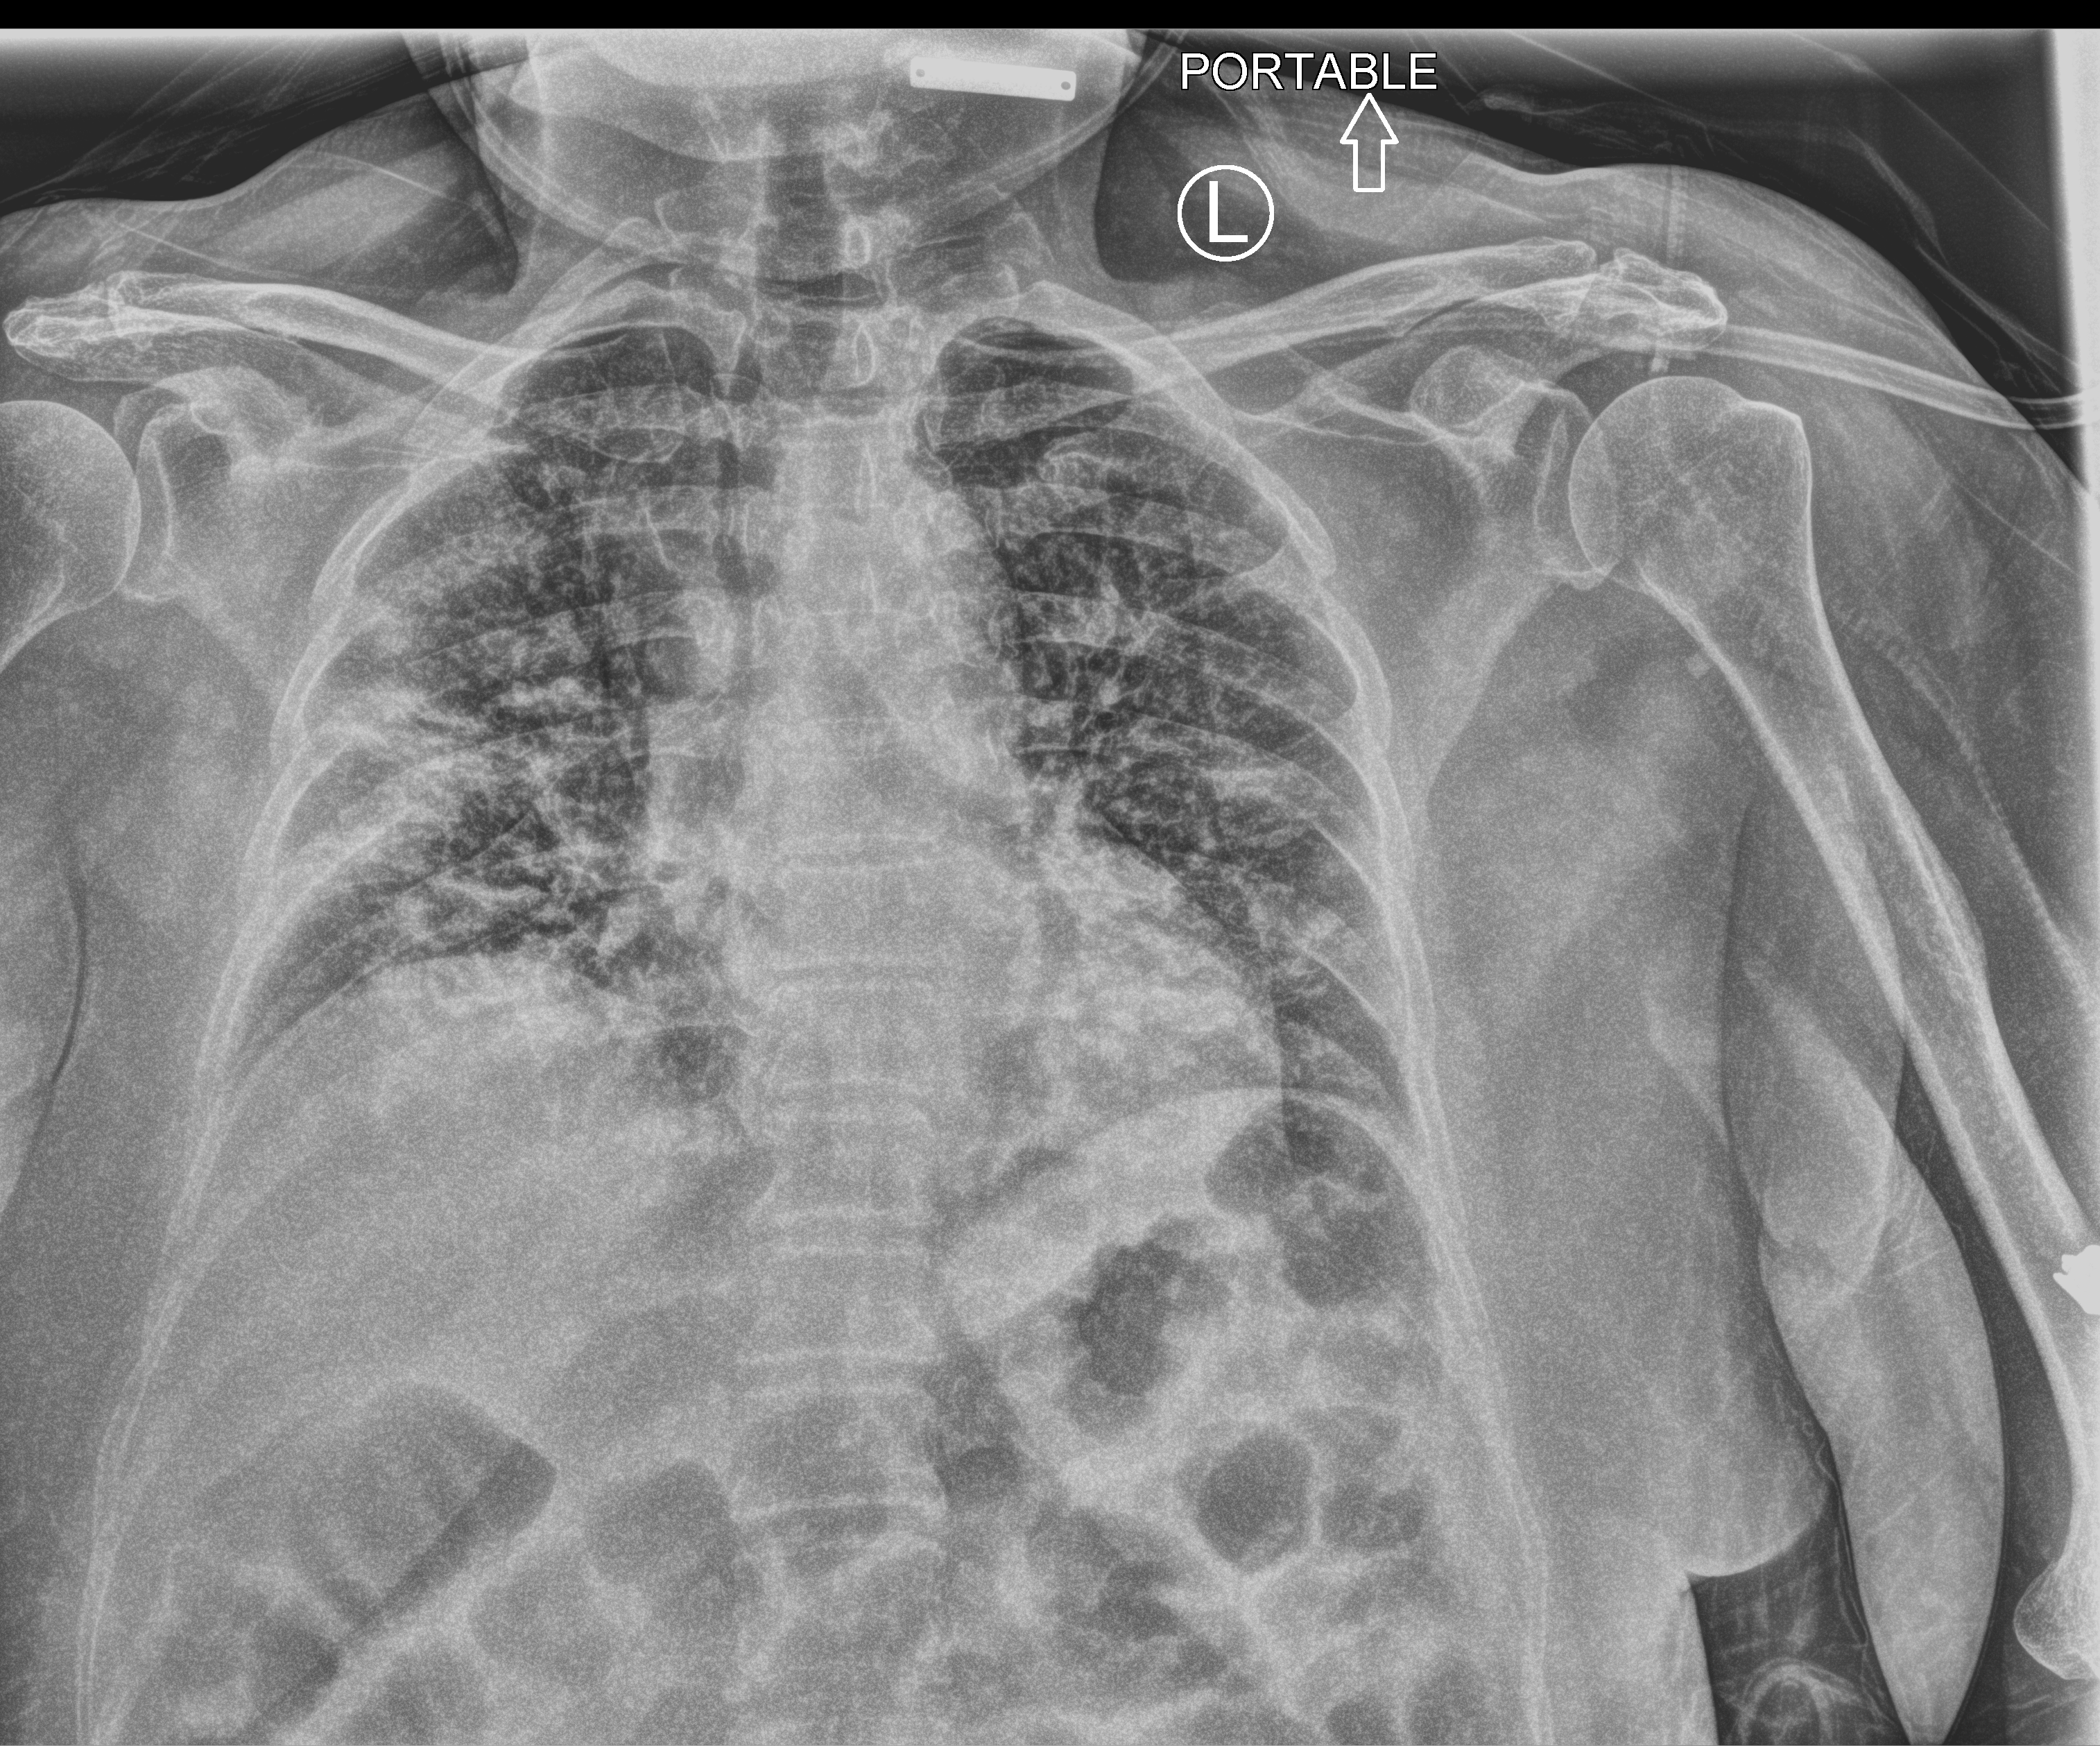
Bedside chest radiograph (computed radiography). Female patient hospitalised with COVID-19, age 60–74 years.
From the hospital-stay record, not from the radiograph (when in the stay this image was taken is not recorded): admitted to intensive care during this hospital stay: no.